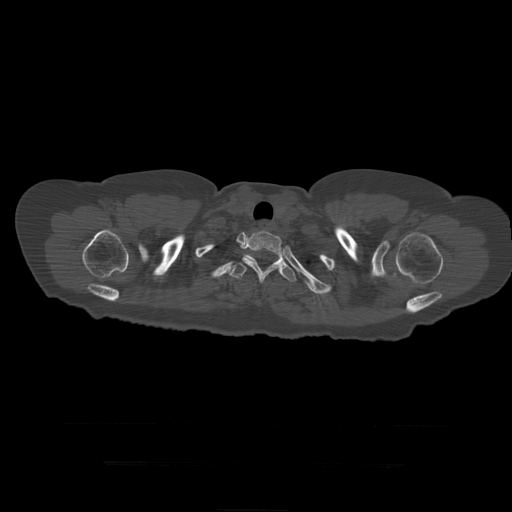
CT including the spine, one axial slice; position 370 of 399 along the scan axis; bone window (W 1800 / L 400 HU); 512 × 512 image matrix, field of view 450 × 450 mm. Patient age 41 years. From the clinical record (not read from this slice): primary cancer: breast.
Structures marked on this image (semi-automatically segmented with operator editing):
- T2 vertebra: bounding box <242,231,282,284> (left, top, right, bottom; pixels)
- T3 vertebra: <228,251,297,283>